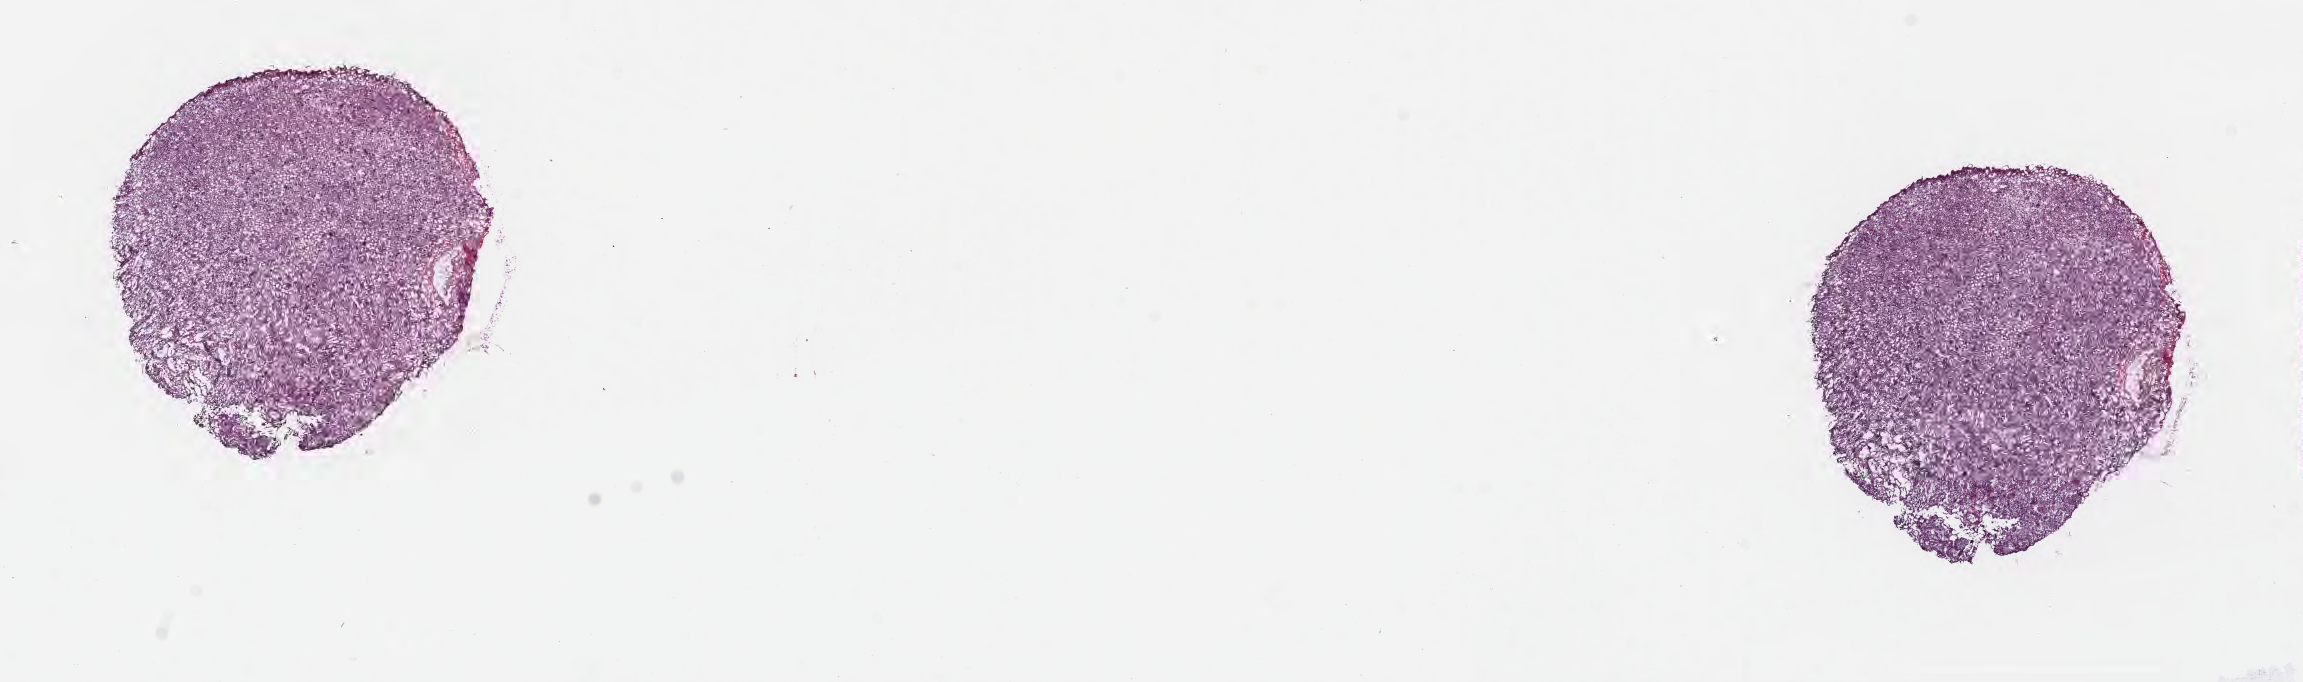
Whole-slide image, H&E stain — shown as a low-resolution overview of the whole scanned area (about 18.6 x 5.5 mm); cryosection; normal-tissue sample (non-tumor) from a patient with nephroblastoma, NOS; site: kidney (left). Male, age 0 years at initial diagnosis. Pathologist review of this section (percent, as recorded): tumor cells 0%, tumor nuclei 0%, stromal cells 15%, necrosis 0%, normal cells 85%. Infiltration values recorded for this section: lymphocyte infiltration 3%, monocyte infiltration 2%, neutrophil infiltration 5%.
• this section: non-tumor tissue sample; the patient's diagnosis is given above
• section: top of the tissue portion